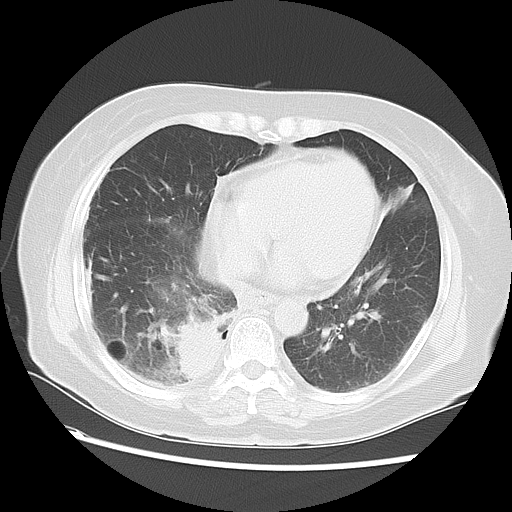
Chest CT, one axial slice. Slice 24 of 57 in the series (ordered by position). Reconstruction kernel LUNG. 120 kVp. Lung window (W 1500 / L -600 HU). 5 mm slice thickness. 512 × 512 image matrix. Female patient, age 69 years. Case-level facts recorded for this patient, not image findings: clinical TNM (as recorded): T2 N1 M1a.
Structures marked on this image (bounding box drawn by a radiologist):
- lung tumour (recorded histology: adenocarcinoma): bounding box [x1, y1, x2, y2] px = [163, 309, 228, 384]